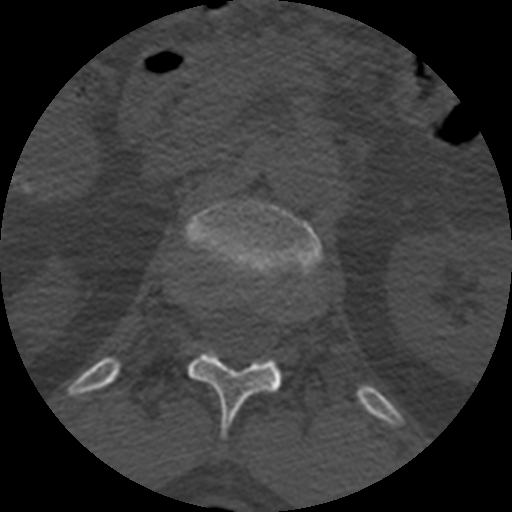
CT including the spine, one axial slice. Position 377 of 399 along the scan axis. Reconstruction kernel STANDARD. 120 kVp. Bone window (W 1800 / L 400 HU). 1.25 mm slice thickness. 512 × 512 image matrix. Patient age 71 years. Case-level facts recorded for this patient, not image findings: primary cancer: prostate.
Annotated regions visible in this slice (semi-automatically segmented with operator editing):
- L1 vertebra: bounding box (x1, y1, x2, y2) in pixels: (183, 200, 323, 281)
- T12 vertebra: (186, 350, 282, 440)